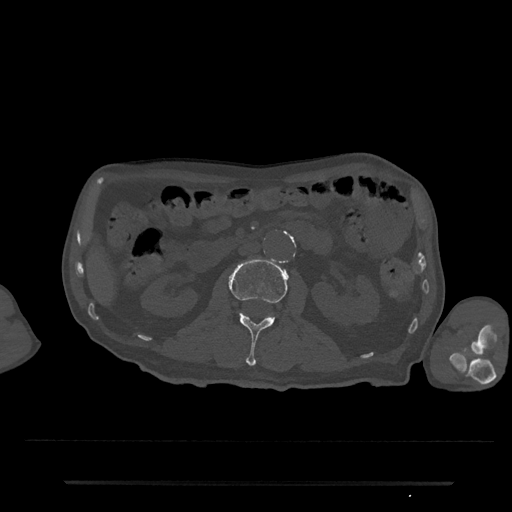
CT including the spine, one axial slice; slice 47 of 797 in the series (ordered by position); reconstruction kernel Br40s/3; bone window (W 1800 / L 400 HU); 0.5 mm slice thickness; 512 × 512 image matrix, field of view 427 × 427 mm. Patient: male, 74 years. From the clinical record (not read from this slice): primary cancer: prostate.
Annotated regions visible in this slice (semi-automatic segmentation, software-assisted and operator-edited):
- L2 vertebra: box from (x=229, y=258) to (x=288, y=366) px